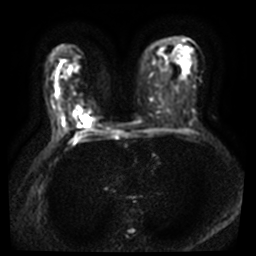
Breast MRI, one axial slice. Slice 27 of 40 in the series (ordered by position). Diffusion-weighted series; image 2 of 4 stored at this slice position (different b-values; order by instance number). 3 T. 256 × 256 image matrix. Female patient.
Annotated regions visible in this slice (outlined manually by an expert reader):
- tumour on diffusion-weighted imaging: bounding box (x1, y1, x2, y2) in pixels: (81, 116, 91, 125)